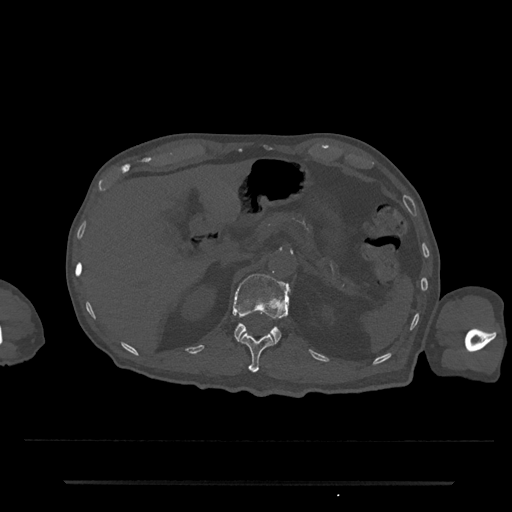
CT including the spine, one axial slice. Slice 166 of 797 in the series (ordered by position). 120 kVp. Bone window (W 1800 / L 400 HU). 0.5 mm slice thickness. 512 × 512 image matrix, field of view 427 × 427 mm. Male patient, age 74 years. From the clinical record (not read from this slice): primary cancer: prostate.
Structures marked on this image (semi-automatic segmentation, software-assisted and operator-edited):
- L1 vertebra: bounding box (x1, y1, x2, y2) in pixels: (232, 274, 291, 344)
- T12 vertebra: (240, 333, 273, 373)